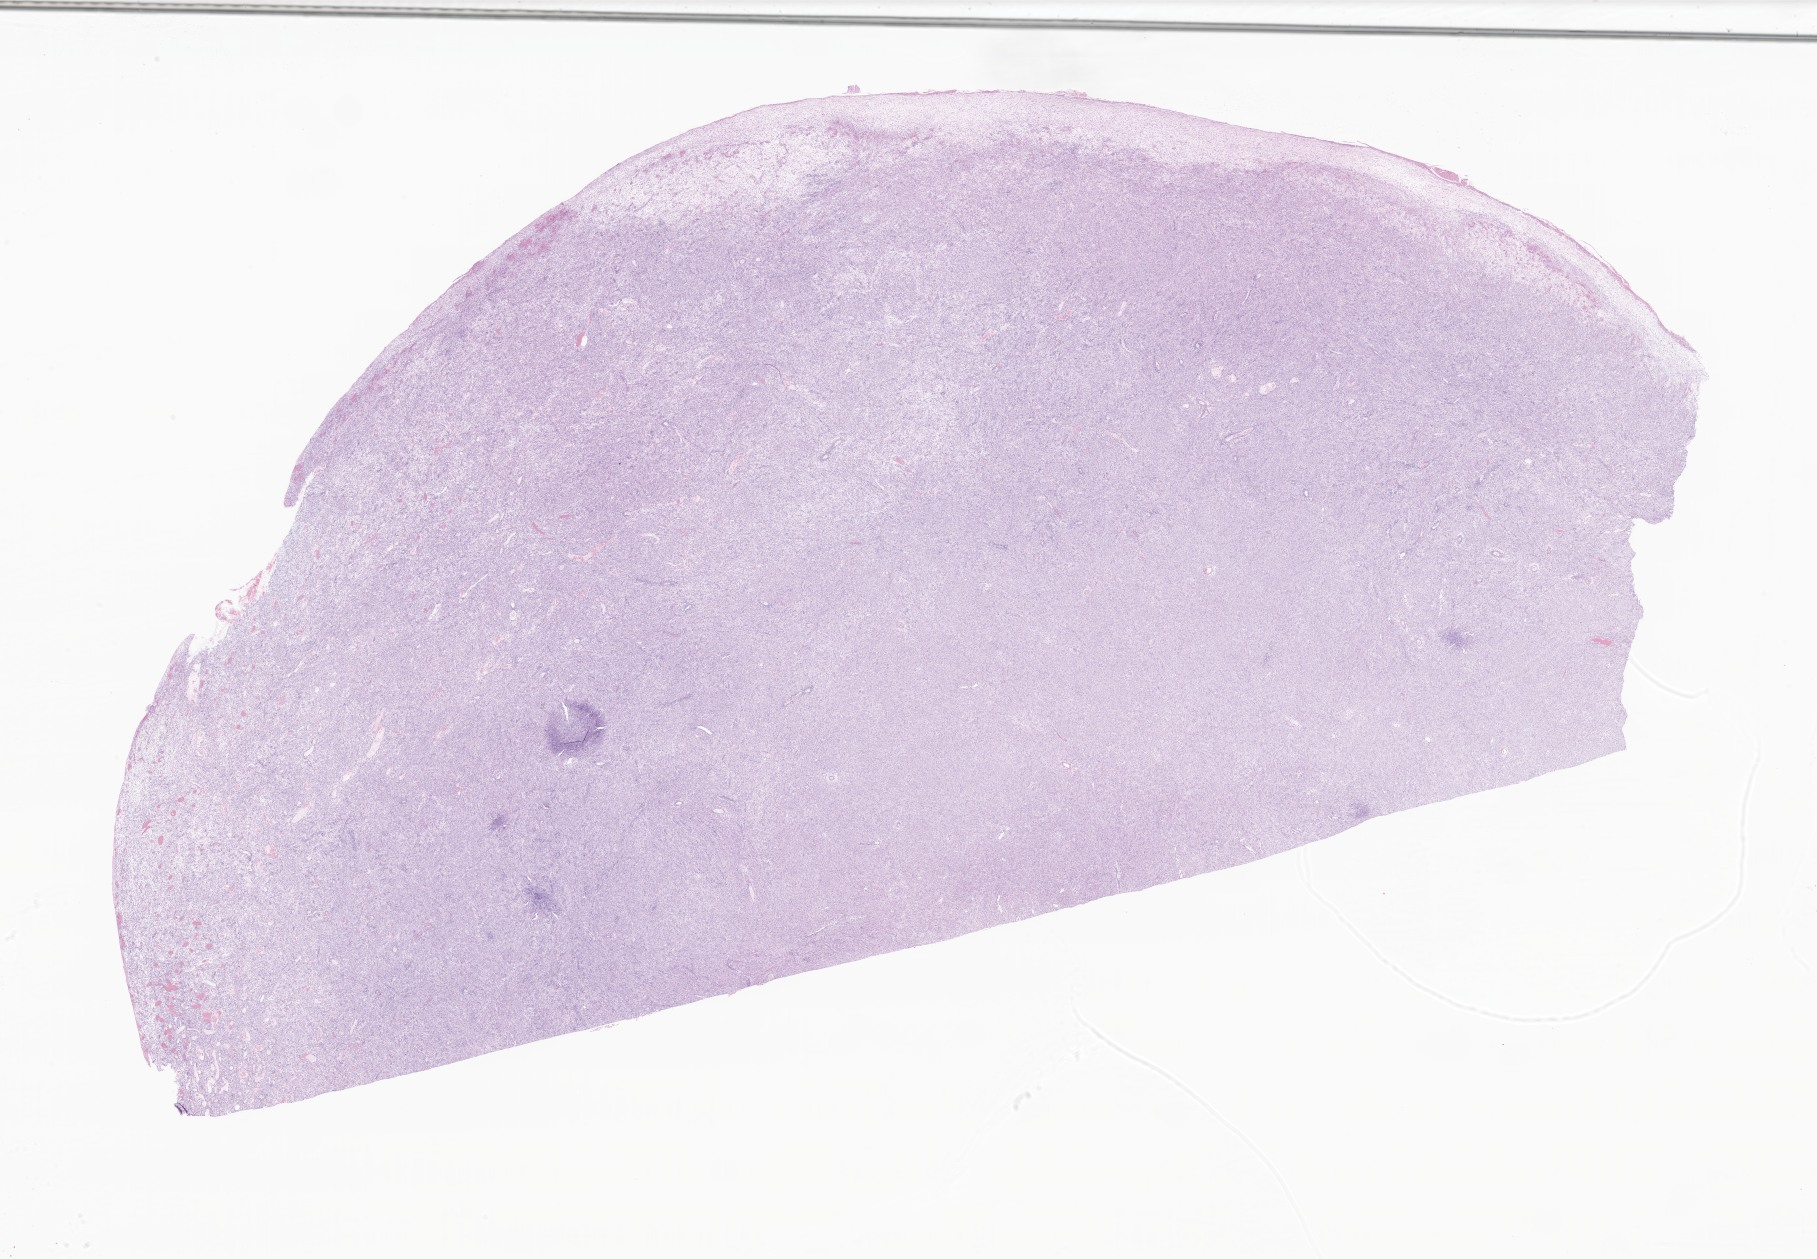
Haematoxylin and eosin whole-slide image of tumor tissue from the cecum, whole scanned area (about 30.7 x 21.2 mm) shown as a low-resolution overview. Formalin-fixed, paraffin-embedded (FFPE) tissue. Male patient, age 587 days (about 1.6 years).
- diagnosis: Myofibroblastic tumor, NOS